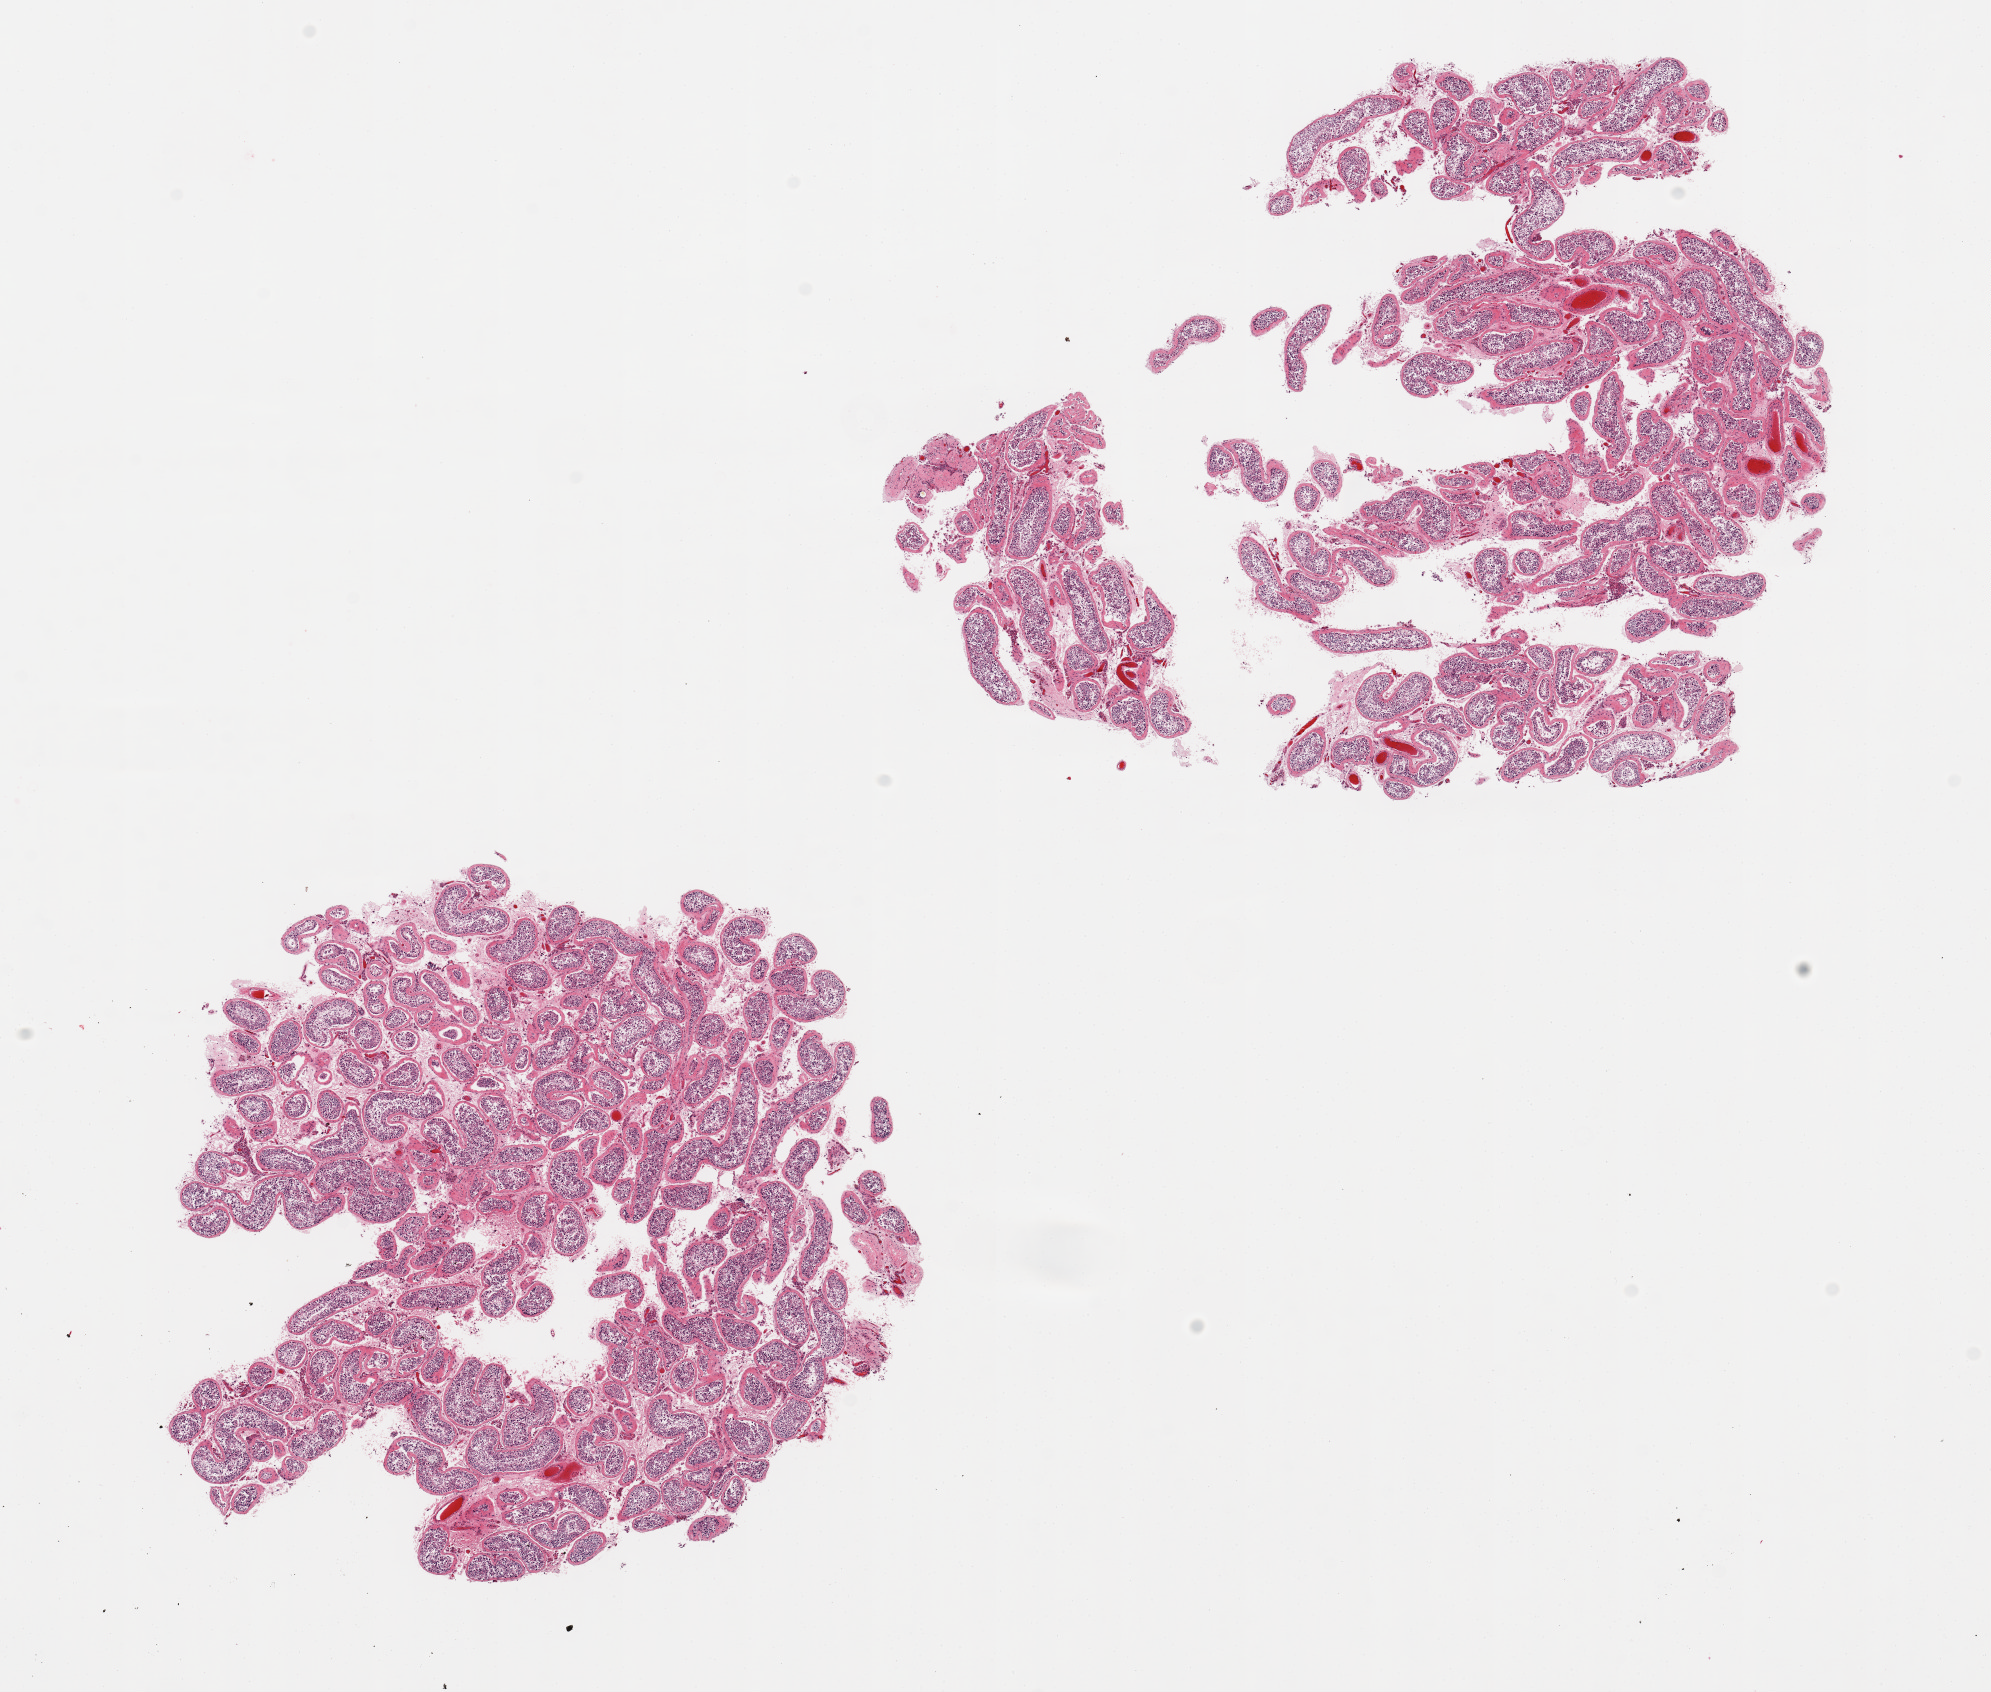
Whole-slide image, haematoxylin and eosin stain, low-resolution overview of the scanned area, about 15.8 x 13.4 mm (slide scanned at 20x), PAXgene-fixed, paraffin-embedded tissue, sampled site (target tissue): testis, tissue donor sample. Donor: male.
Reviewer comment on this tissue sample: 2 pieces; spermatogenesis is present, few hyalinized tubules.